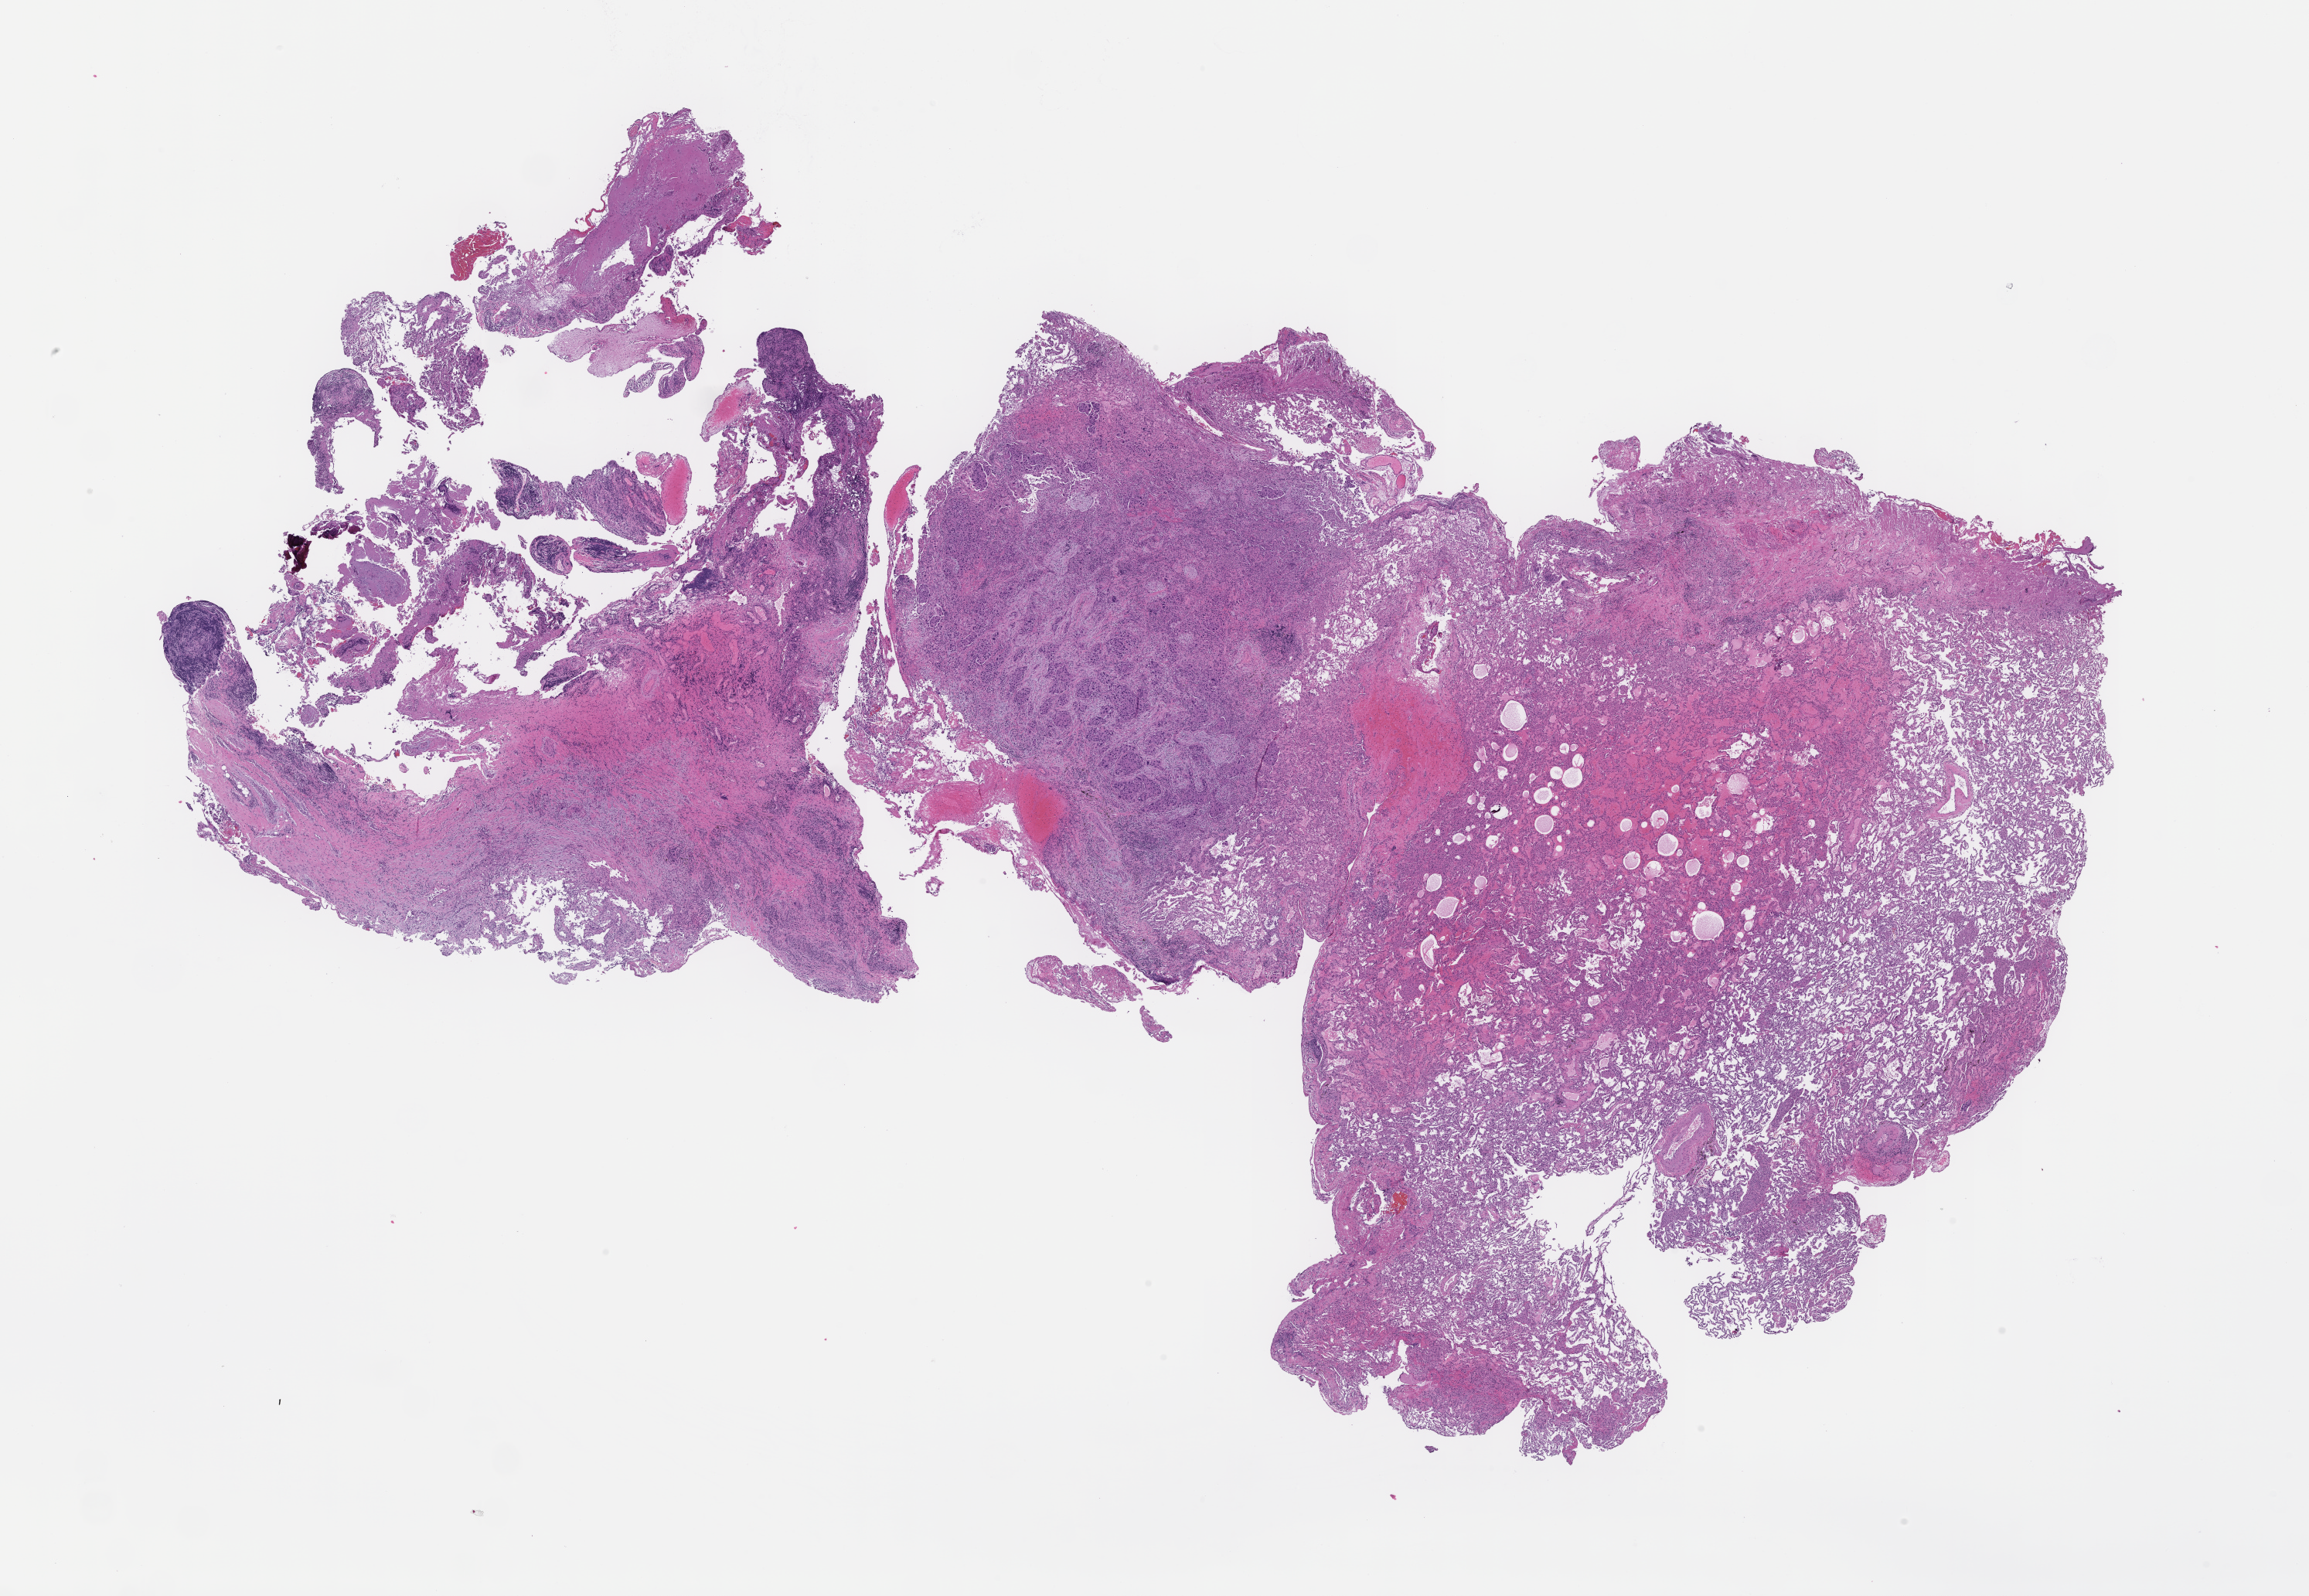
Digitized haematoxylin and eosin-stained section, low-resolution overview of the scanned area, about 24.1 x 16.7 mm. FFPE section. Tissue site: lung. Archival tissue. Patient sex: male.
- this section: primary tumour tissue
- diagnosis: Non-Small Cell Lung Carcinoma